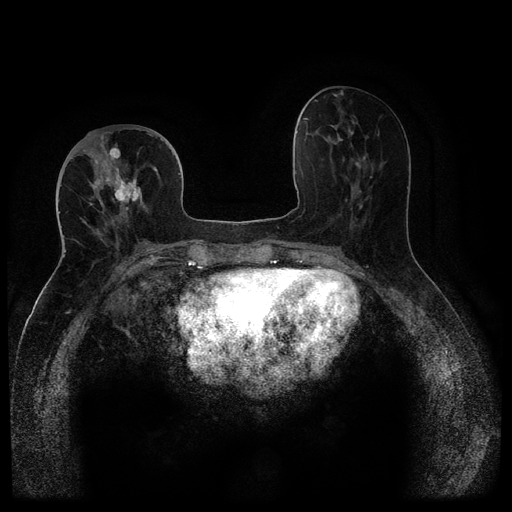
Breast MRI (dynamic contrast-enhanced, multi-phase), one axial slice. Position 45 of 116 along the scan axis. Dynamic contrast-enhanced series, time point 2 of 5 at this slice position (early post-contrast). 1.5 T. TE 2.6 ms, TR 5.4 ms. 512 × 512 image matrix, field of view 340 × 340 mm. Female patient, age 68 years.
Outlined on this slice (semi-automatic segmentation, software-assisted and operator-edited):
- breast lesion (labelled 'tumour' in the annotation; benign lesions carry a separate 'benign' label): bounding box [x1, y1, x2, y2] px = [110, 161, 143, 211]